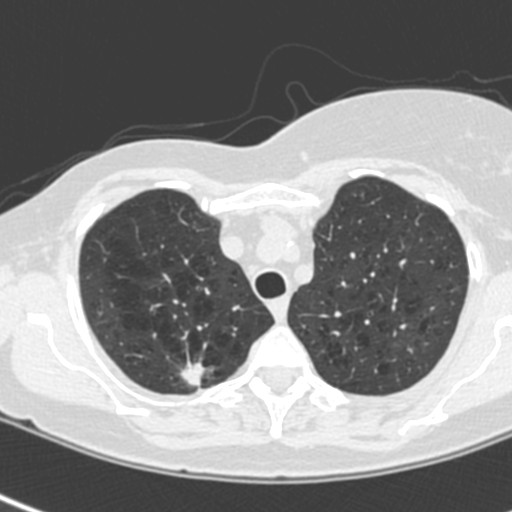
Low-dose screening chest CT, one axial slice; slice 179 of 214 in the series (ordered by position); 120 kVp; lung window (W 1500 / L -600 HU); 1.3 mm slice thickness; 512 × 512 image matrix.
Structures marked on this image (outlined manually by an expert reader):
- lesion 1 (tumor, upper lobe of right lung): bounding box <180,362,204,388> (left, top, right, bottom; pixels)